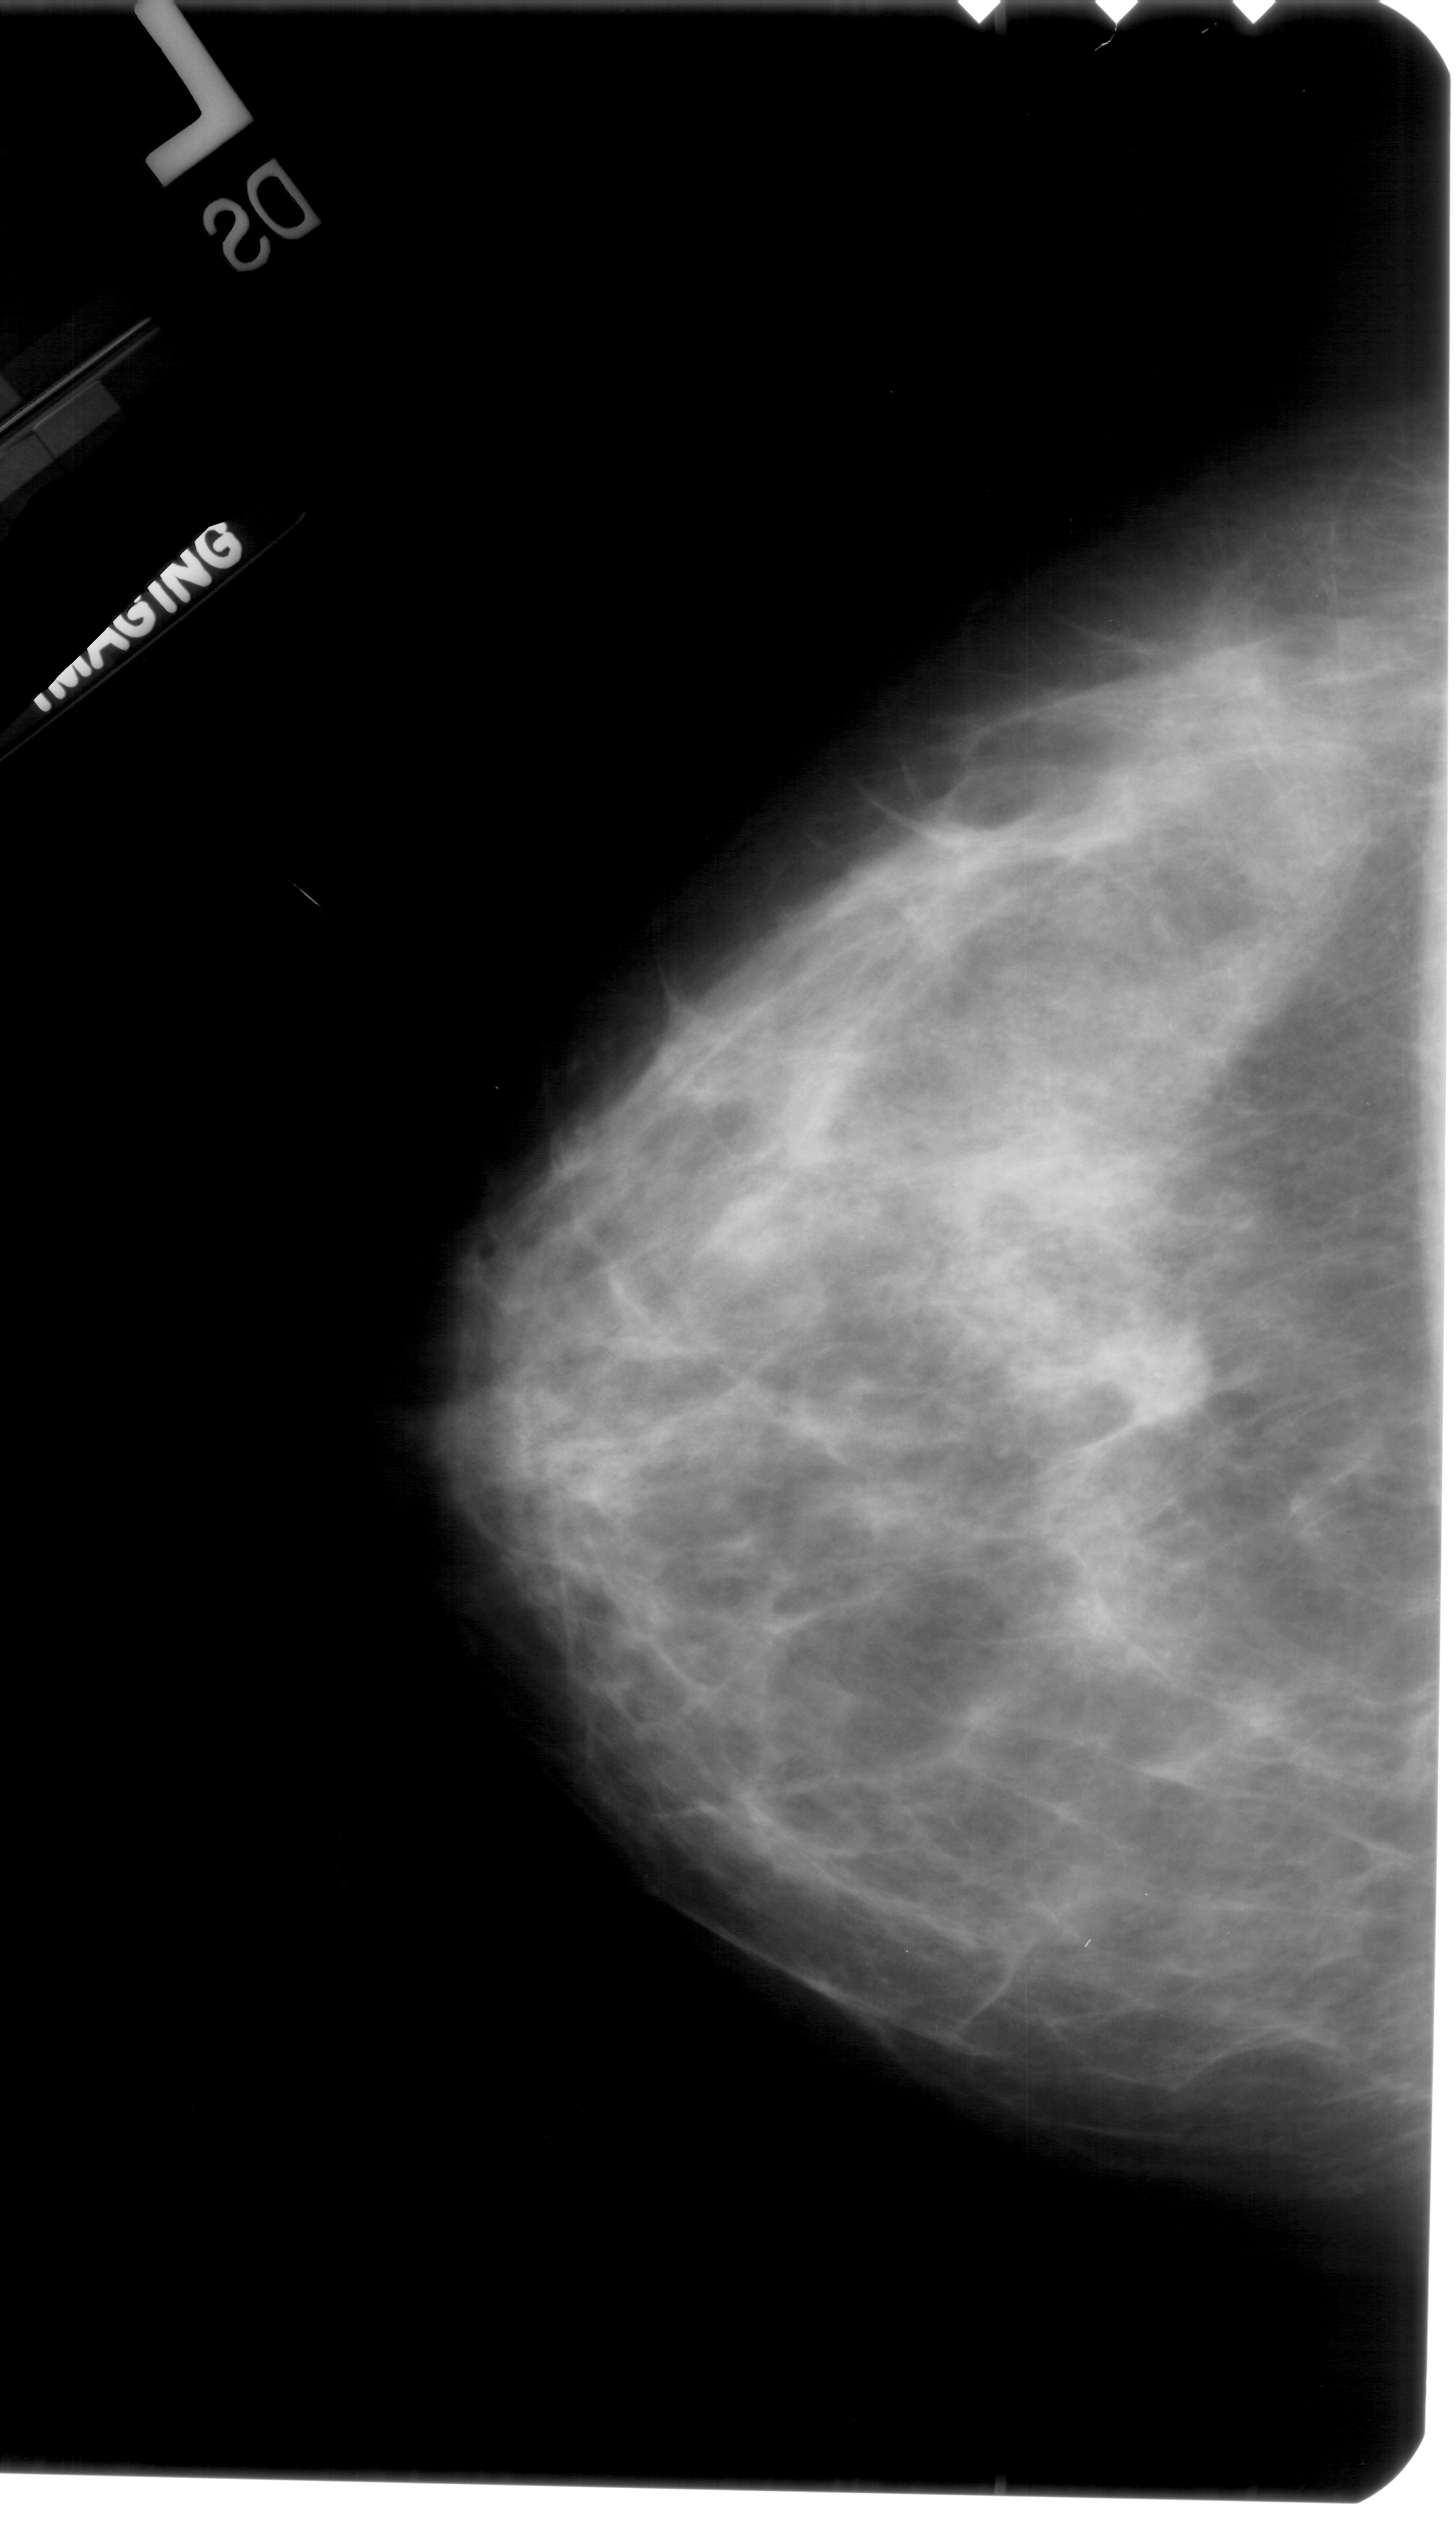
Scanned film-screen mammogram; left breast; CC view; BI-RADS breast density category 4 (scale 1–4).
Abnormality record for this image: mass, shape focal asymmetric density, margins ill defined; BI-RADS assessment category 4; pathology (as recorded): malignant.